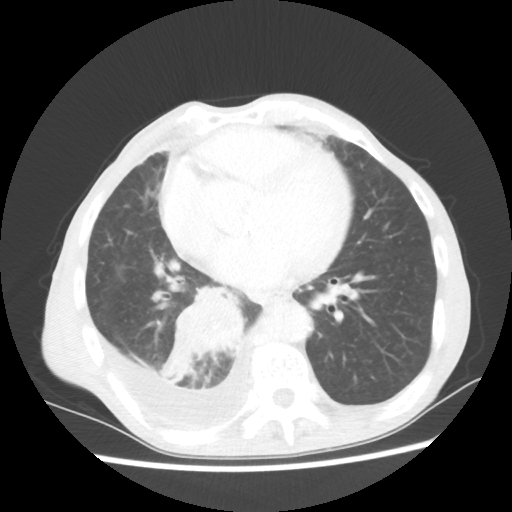
Chest CT, one axial slice; slice 25 of 60 in the series (ordered by position); 80 kVp; lung window (W 1500 / L -600 HU); 512 × 512 image matrix. Male patient, age 76 years. From the clinical record (not read from this slice): clinical TNM (as recorded): T3 N3 M1a.
Annotated regions visible in this slice (rectangle marked by the reading radiologist):
- lung tumour (recorded histology: squamous cell carcinoma): bounding box <158,284,252,386> (left, top, right, bottom; pixels)